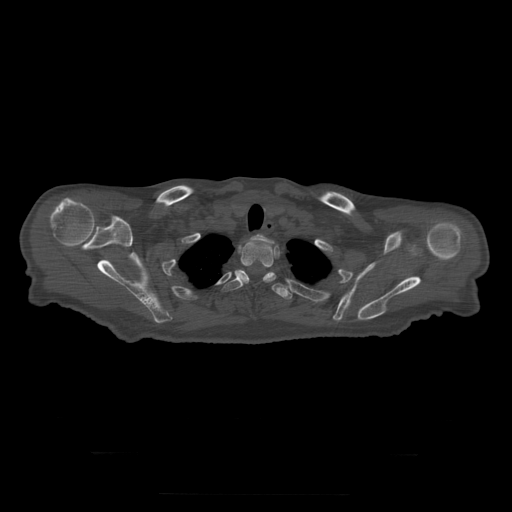
CT including the spine, one axial slice; position 268 of 397 along the scan axis; 120 kVp; bone window (W 1800 / L 400 HU); 512 × 512 image matrix, field of view 510 × 510 mm. Patient age 73 years. Case-level facts recorded for this patient, not image findings: primary cancer: prostate.
Structures marked on this image (semi-automatic segmentation, software-assisted and operator-edited):
- T1 vertebra: bounding box (x1, y1, x2, y2) in pixels: (252, 235, 274, 244)
- T2 vertebra: (241, 240, 276, 283)
- T3 vertebra: (222, 270, 293, 299)